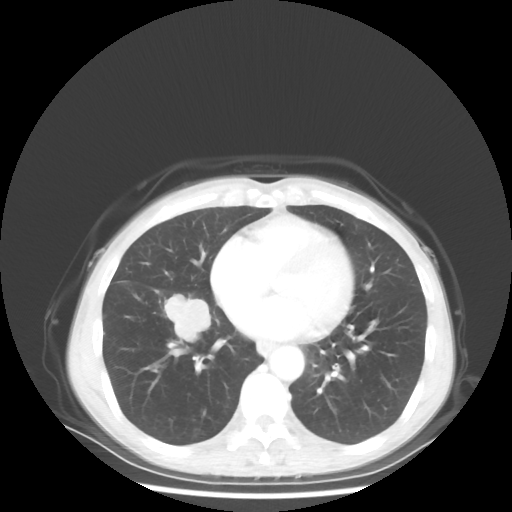
Chest CT, one axial slice; position 21 of 56 along the scan axis; reconstruction kernel STANDARD; 80 kVp; lung window (W 1500 / L -600 HU); 512 × 512 image matrix, field of view 360 × 360 mm. Patient: female, 57 years. Case-level facts recorded for this patient, not image findings: clinical TNM (as recorded): T1c N3 M1a.
Structures marked on this image (bounding box drawn by a radiologist):
- lung tumour (recorded histology: adenocarcinoma): bounding box (x1, y1, x2, y2) in pixels: (166, 291, 212, 345)